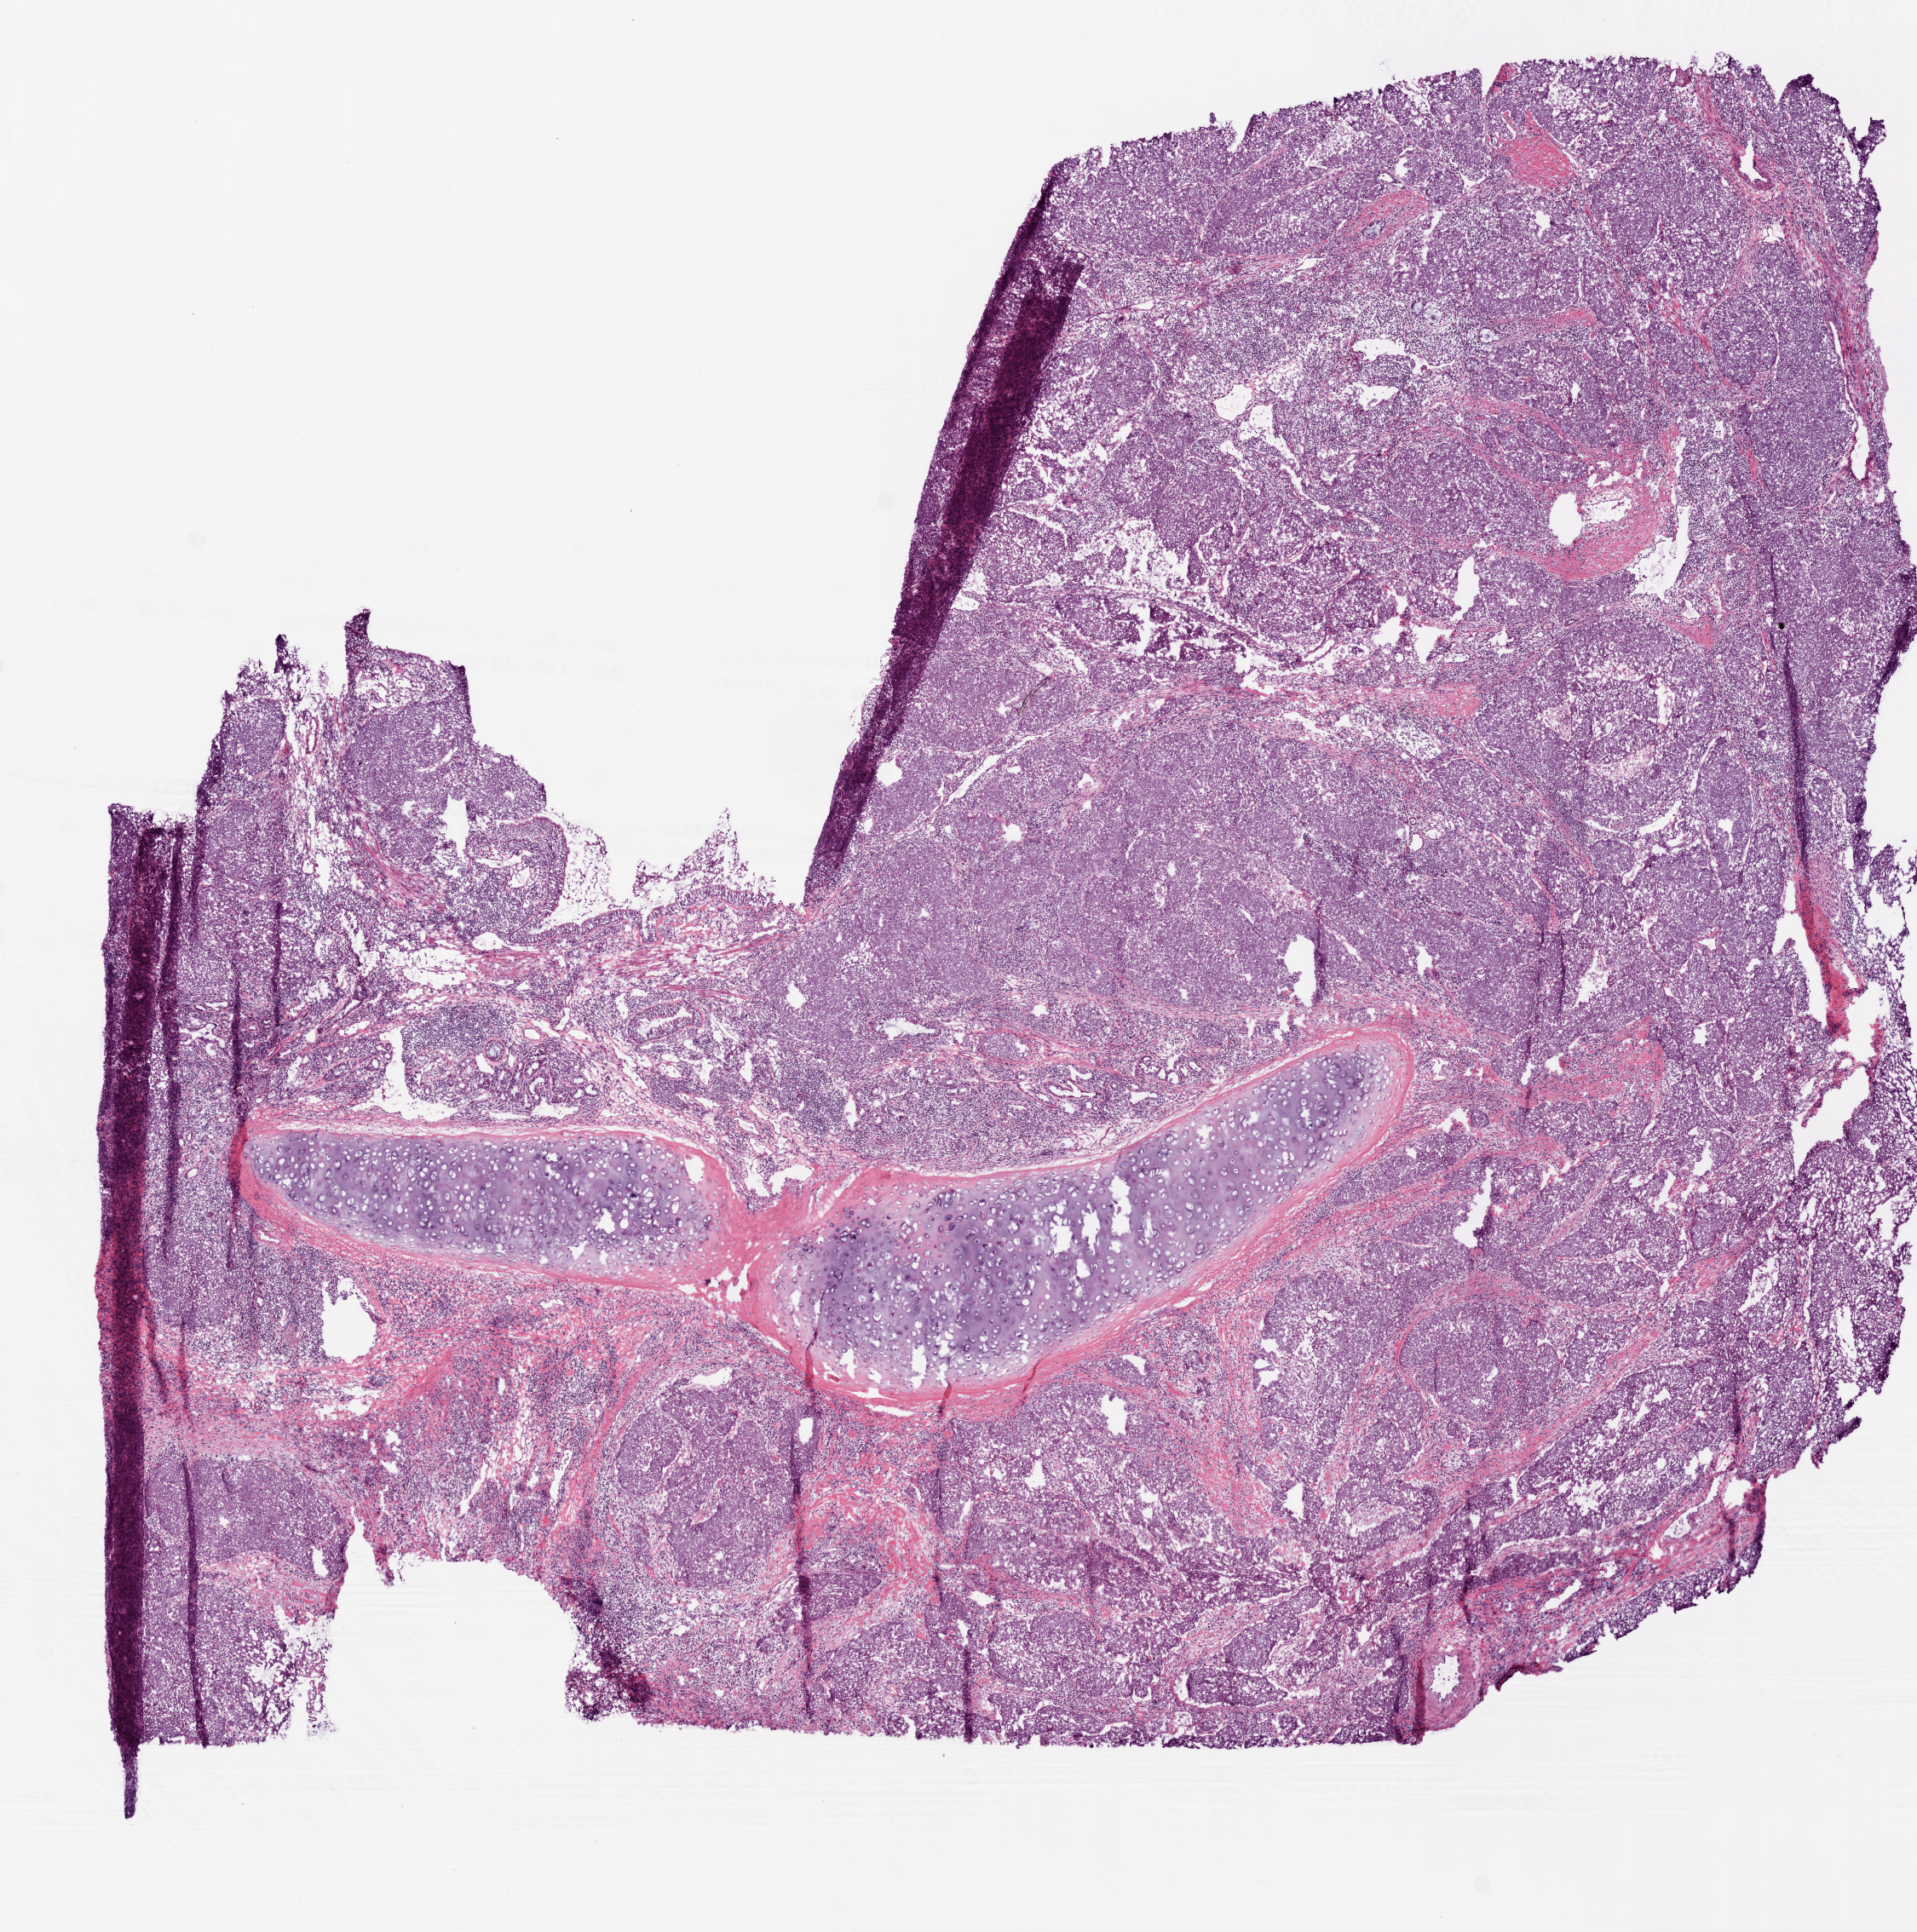
Whole-slide histology image, H&E — whole scanned area (about 9.0 x 9.1 mm, acquisition: 20x scan) shown as a low-resolution overview, frozen section, sample: primary tumour, lung. Male, age 53 years at initial diagnosis. Slide review estimates, as recorded: tumour cells 77%, tumour nuclei 75%, normal cells 8%, stromal cells 10%, necrosis 5%.
Laterality: right. Histologic diagnosis: Adenocarcinoma, NOS. AJCC pathologic stage: IIIA.